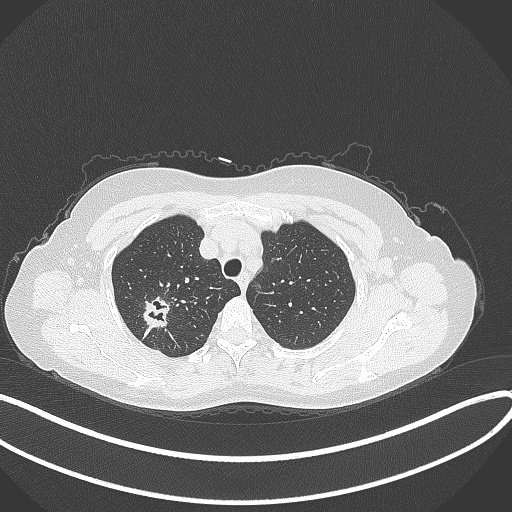
Chest CT, one axial slice. Reconstruction kernel B70f. 120 kVp. Lung window (W 1500 / L -600 HU). 1 mm slice thickness. 512 × 512 image matrix. Patient: female, 50 years. Case-level facts recorded for this patient, not image findings: clinical TNM (as recorded): T1c N0 M0.
Structures marked on this image (rectangle marked by the reading radiologist):
- lung tumour (recorded histology: adenocarcinoma): bounding box [x1, y1, x2, y2] px = [139, 292, 173, 333]